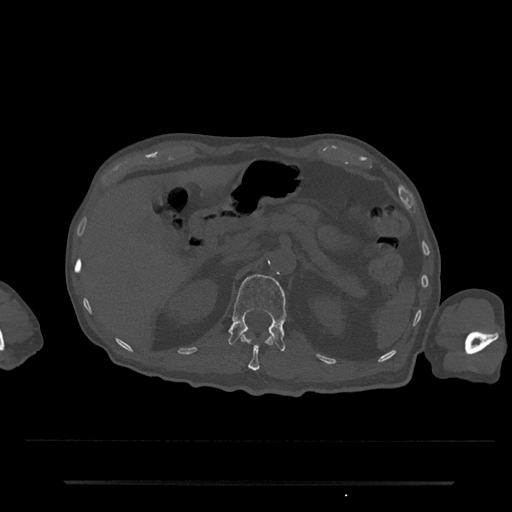
CT including the spine, one axial slice. Position 153 of 797 along the scan axis. Reconstruction kernel Br40s/3. 120 kVp. Bone window (W 1800 / L 400 HU). 512 × 512 image matrix, field of view 427 × 427 mm. Patient: male, 74 years. Case-level facts recorded for this patient, not image findings: primary cancer: prostate.
Structures marked on this image (semi-automatically segmented with operator editing):
- L1 vertebra: bounding box <228,274,287,352> (left, top, right, bottom; pixels)
- T12 vertebra: <241,334,273,371>